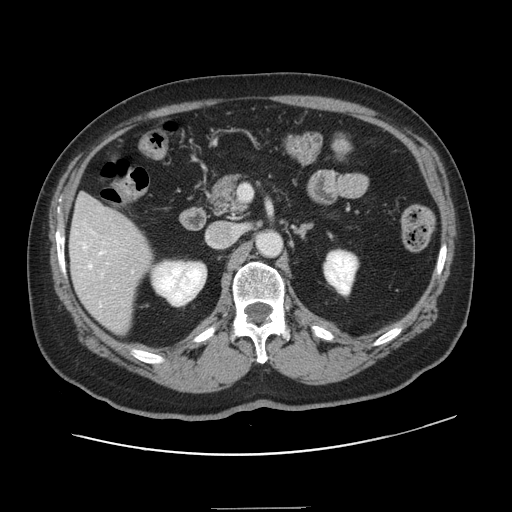
Contrast-enhanced abdominal CT, one axial slice. Position 69 of 143 along the scan axis. 120 kVp. Soft-tissue window (W 400 / L 40 HU). 512 × 512 image matrix, field of view 402 × 402 mm. Male patient, age 62 years. From the clinical record (not read from this slice): diagnosis: colorectal cancer liver metastases, imaged before liver resection; multiple liver metastases: yes; largest metastasis: 2.7 cm; chemotherapy before resection: yes.
Annotated regions visible in this slice (manually delineated by an expert):
- hepatic veins: box from (x=83, y=244) to (x=104, y=305) px
- liver: (x=70, y=195)–(x=153, y=333)
- planned liver remnant (the part of the liver to remain after resection): (x=75, y=195)–(x=110, y=218)
- portal vein (with intrahepatic branches): (x=103, y=241)–(x=133, y=273)